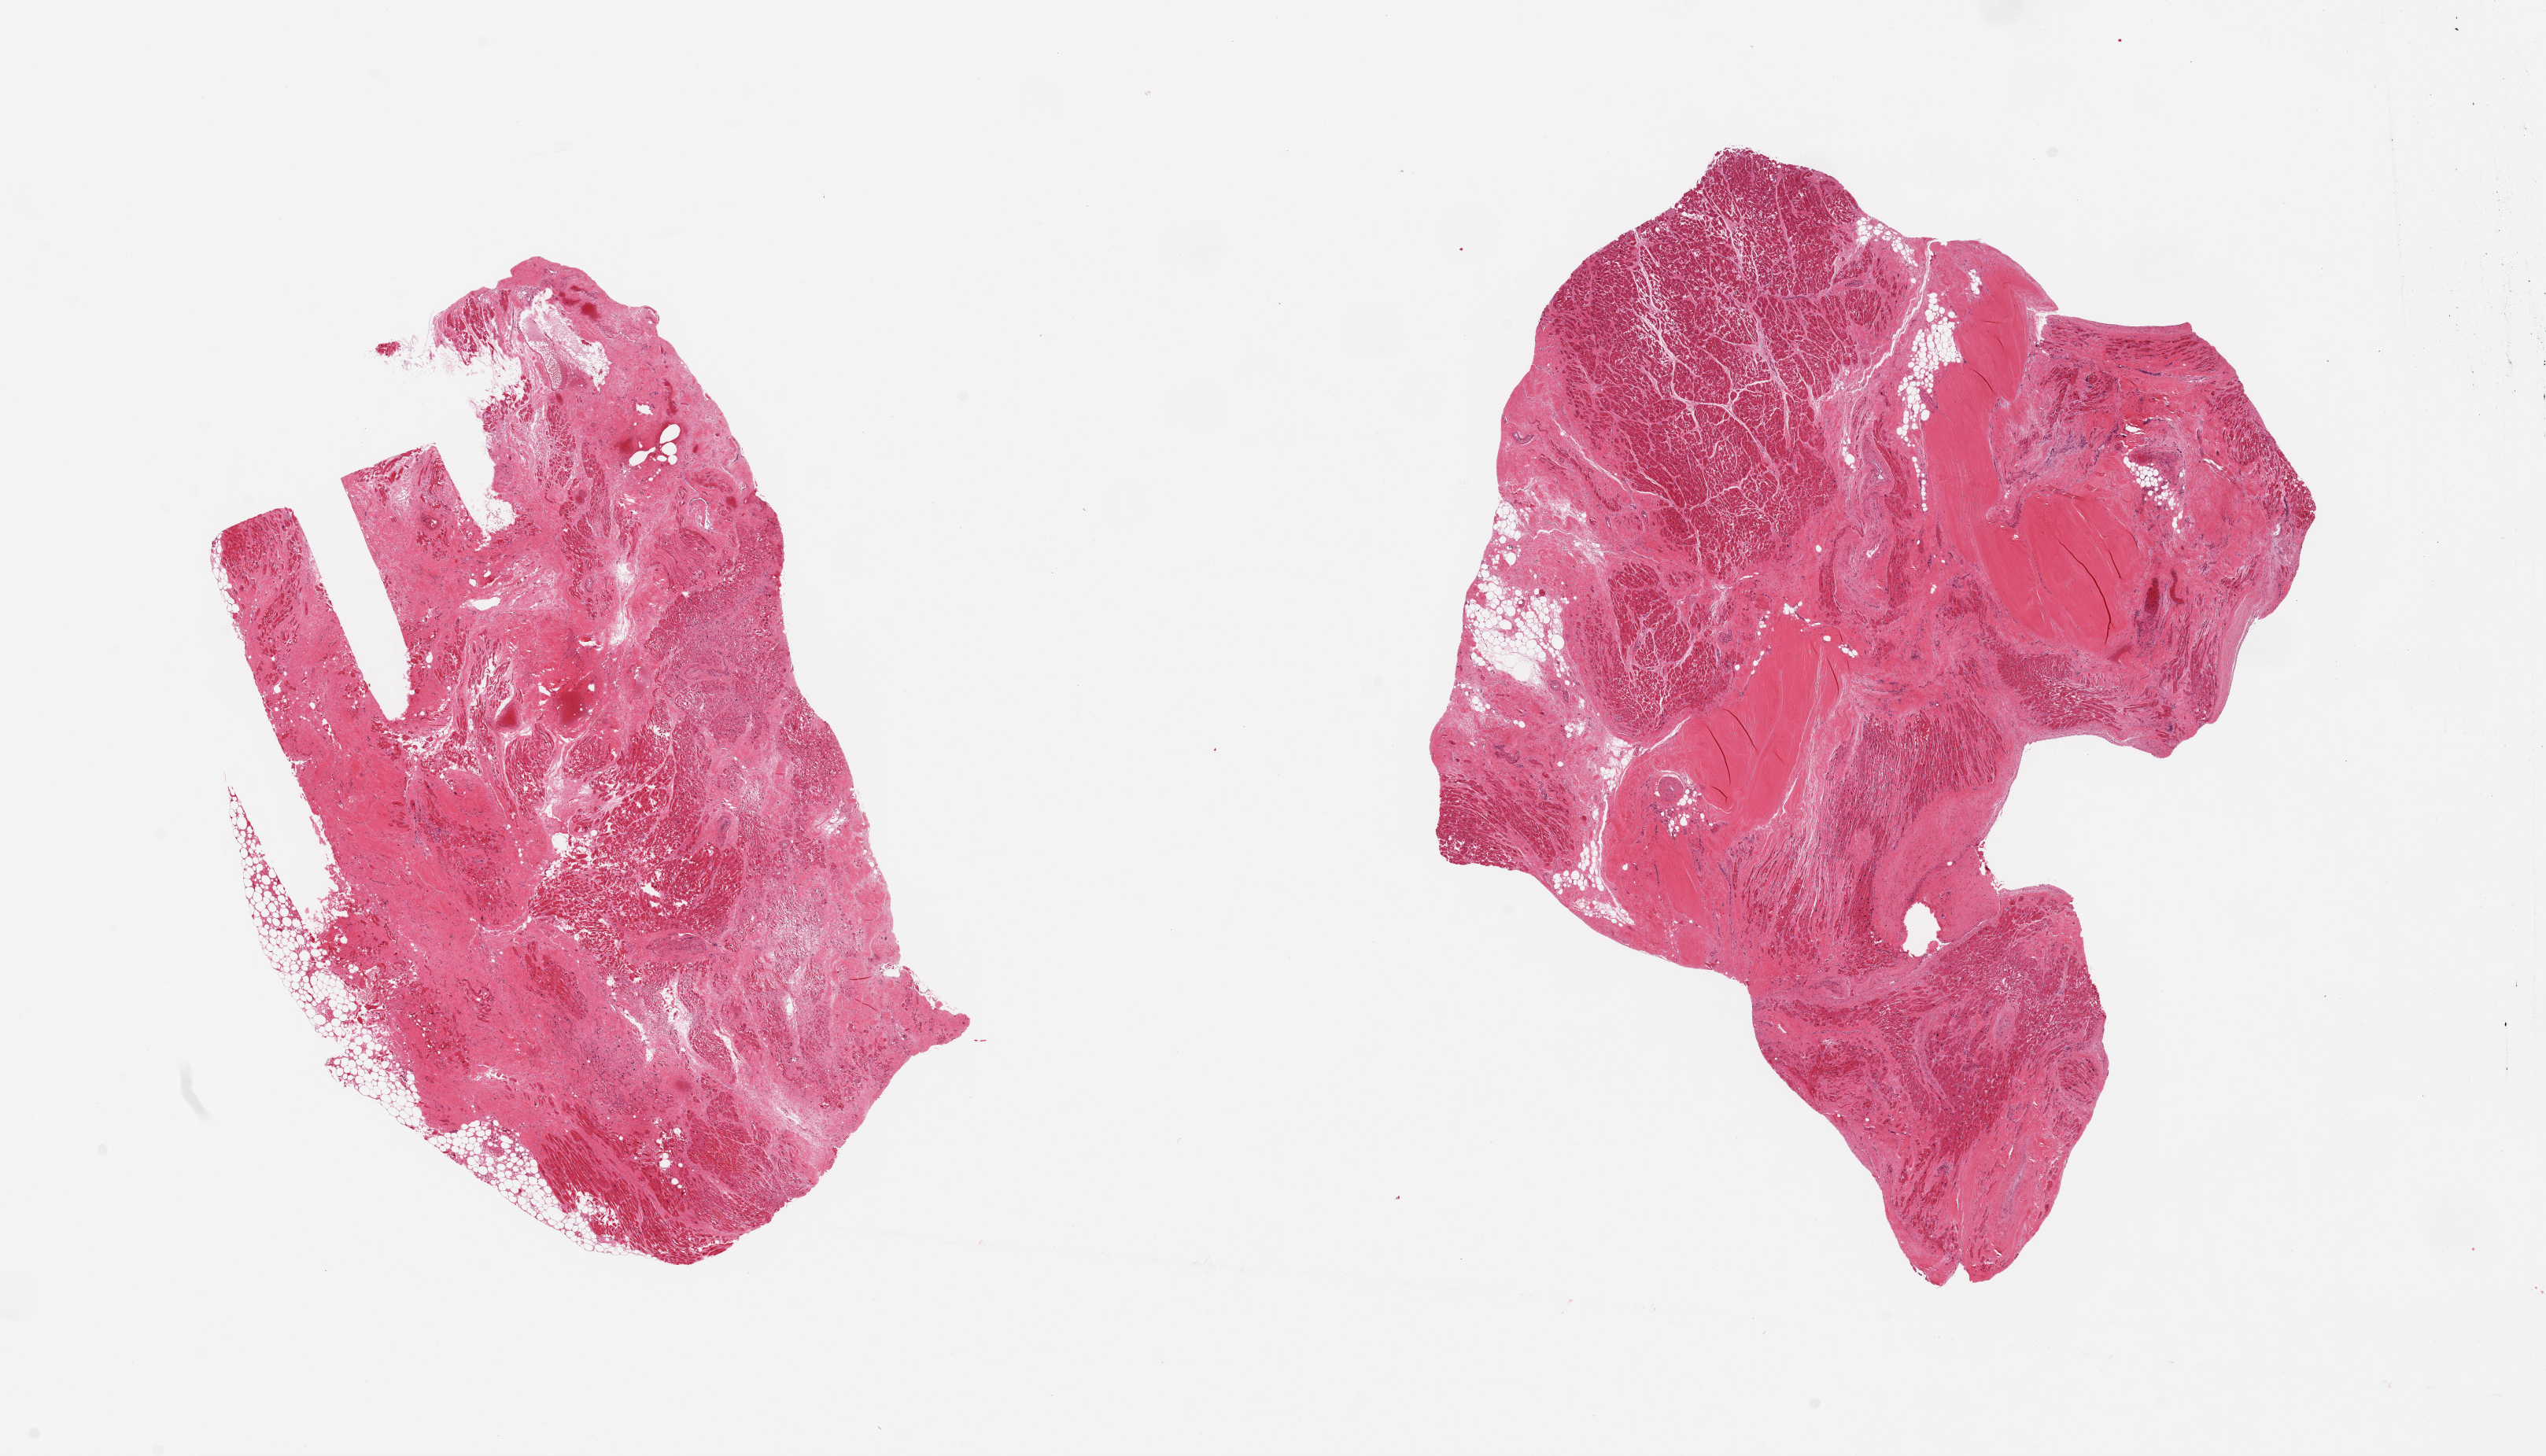
Whole-slide image, haematoxylin and eosin stain, brightfield — a low-resolution overview of the entire scanned area, about 25.6 x 14.6 mm. PAXgene-fixed paraffin-embedded (PFPE) section. Sampled site (target tissue): heart. Donor tissue sample. Donor: male.
- pathologist's review note for this sample: 2 pieces; extensive scarring consistent with old infarcts, focus of coagulative necrosis compatible with recent infarct, hypertrophy